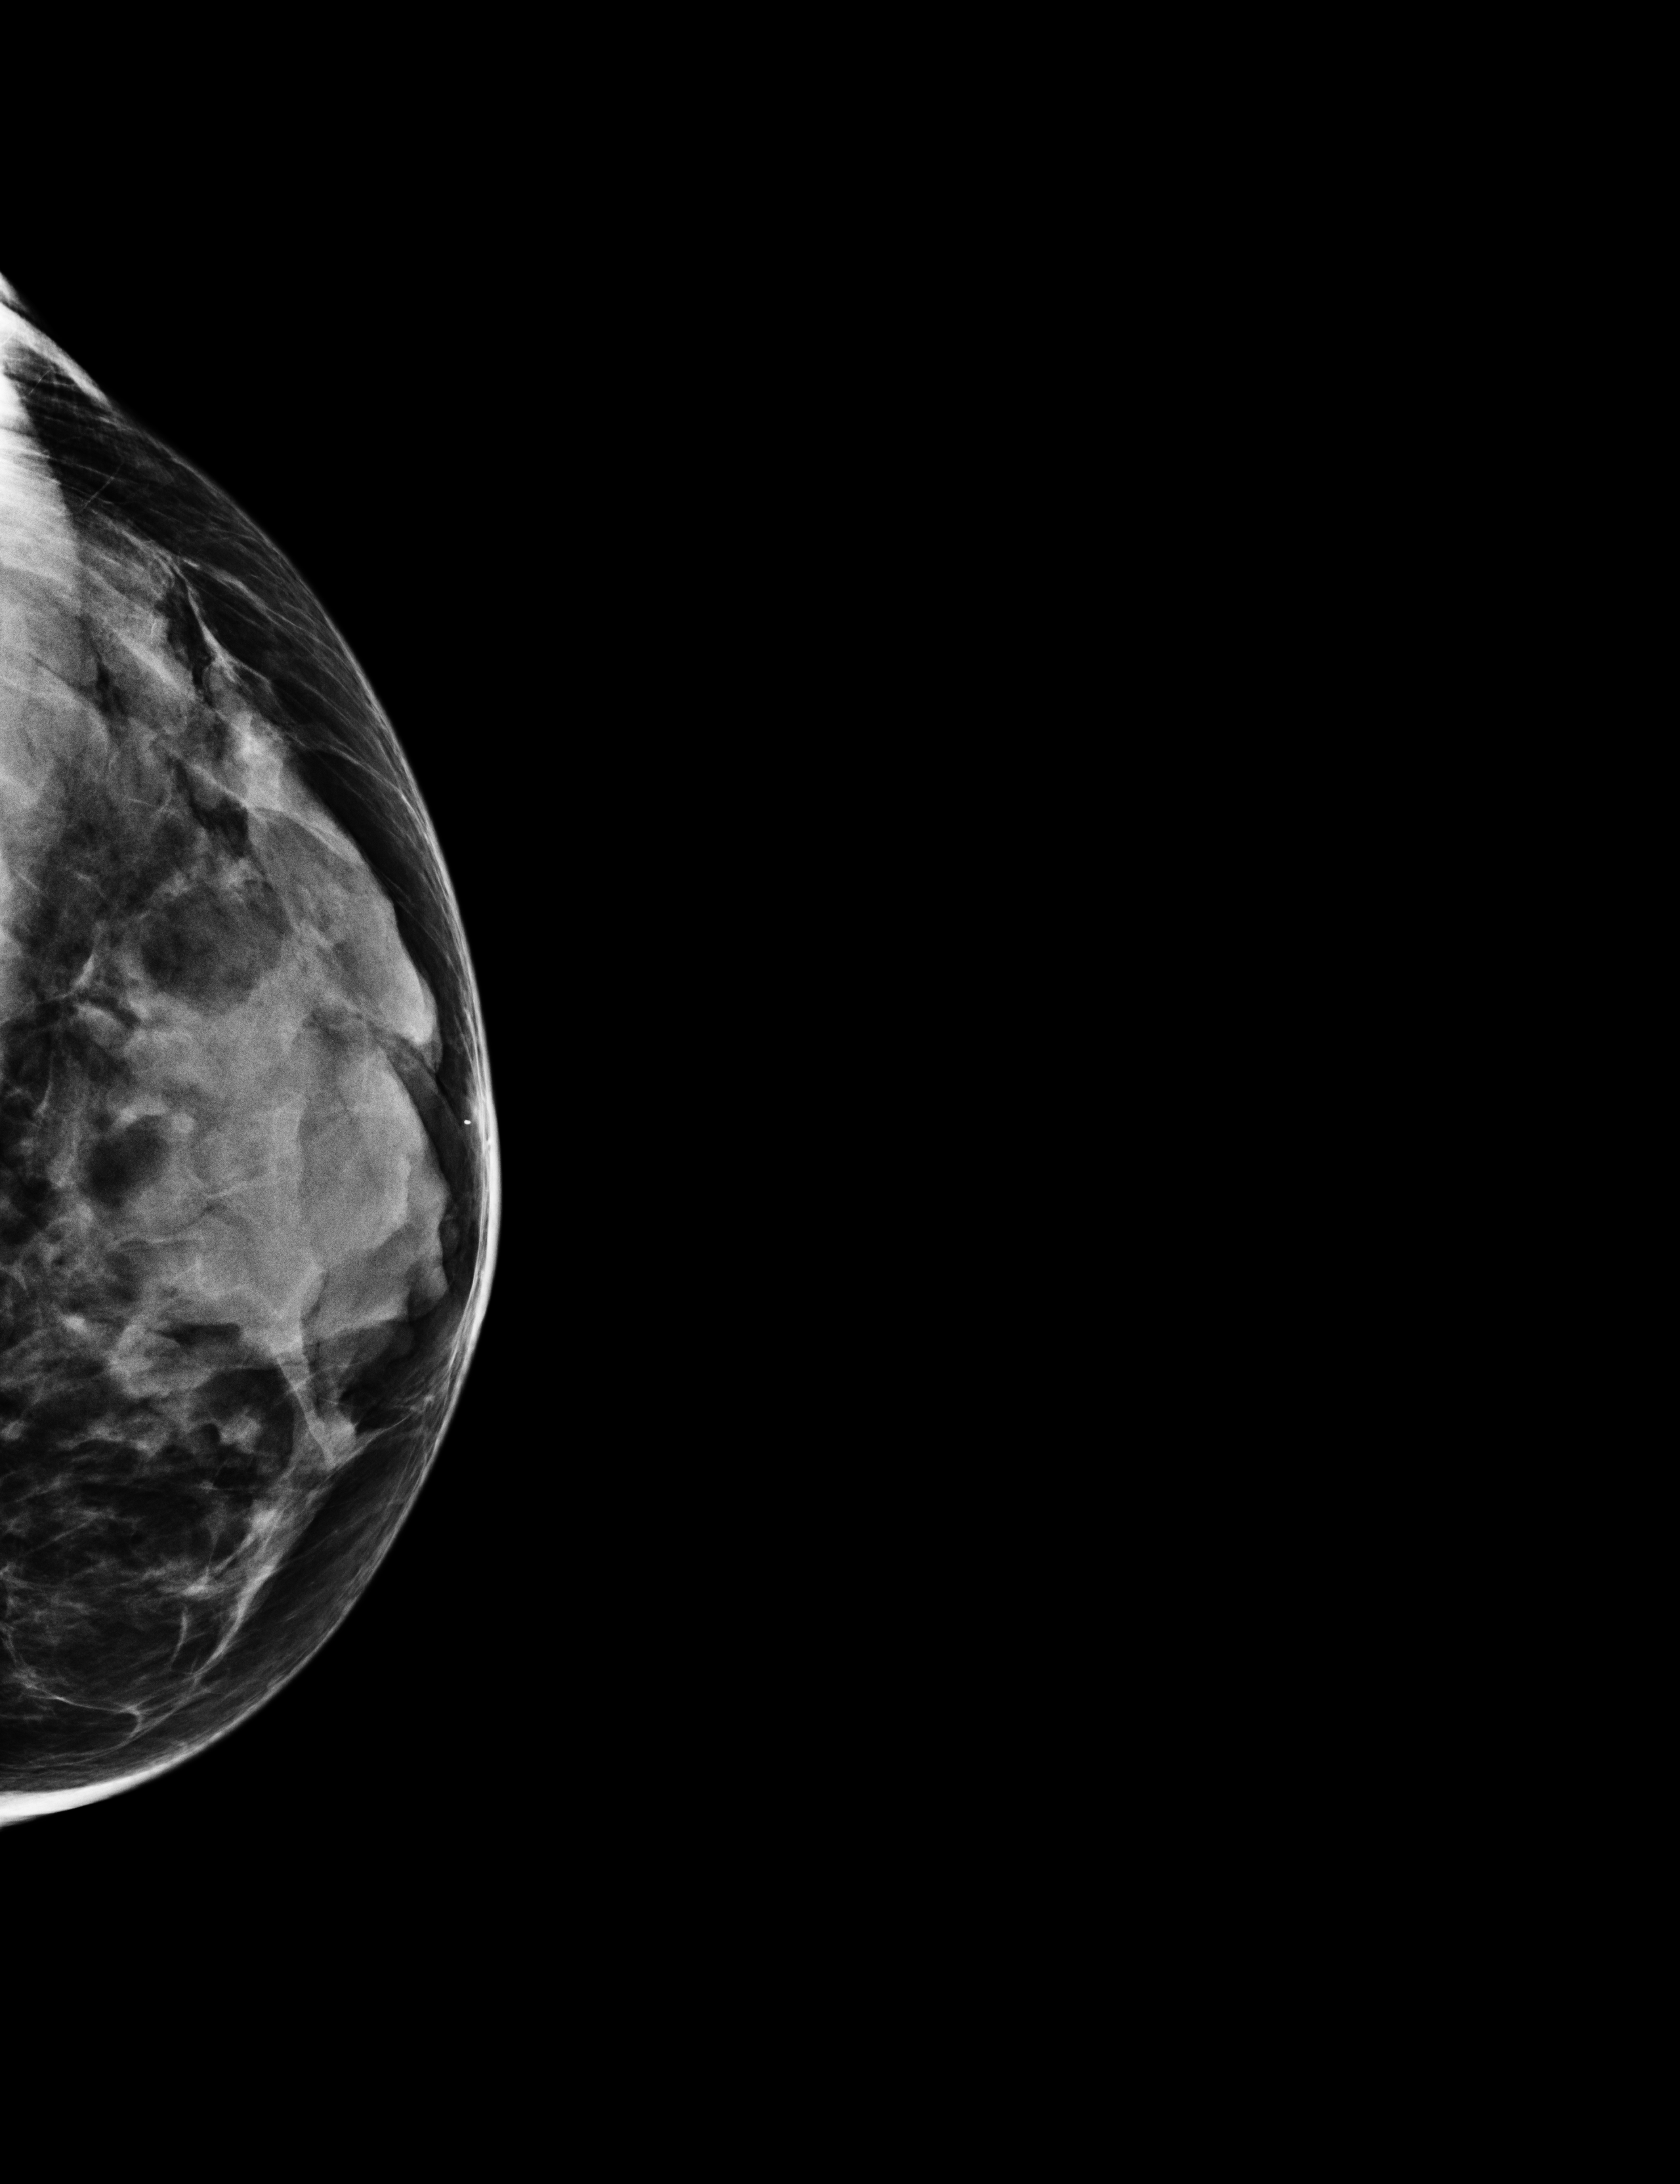
Annual screening mammography examination; system: Selenia Dimensions. Patient: female, 59 years.
Image type: full-field digital mammogram. Breast: left. Projection: laterally exaggerated craniocaudal (XCCL) view.